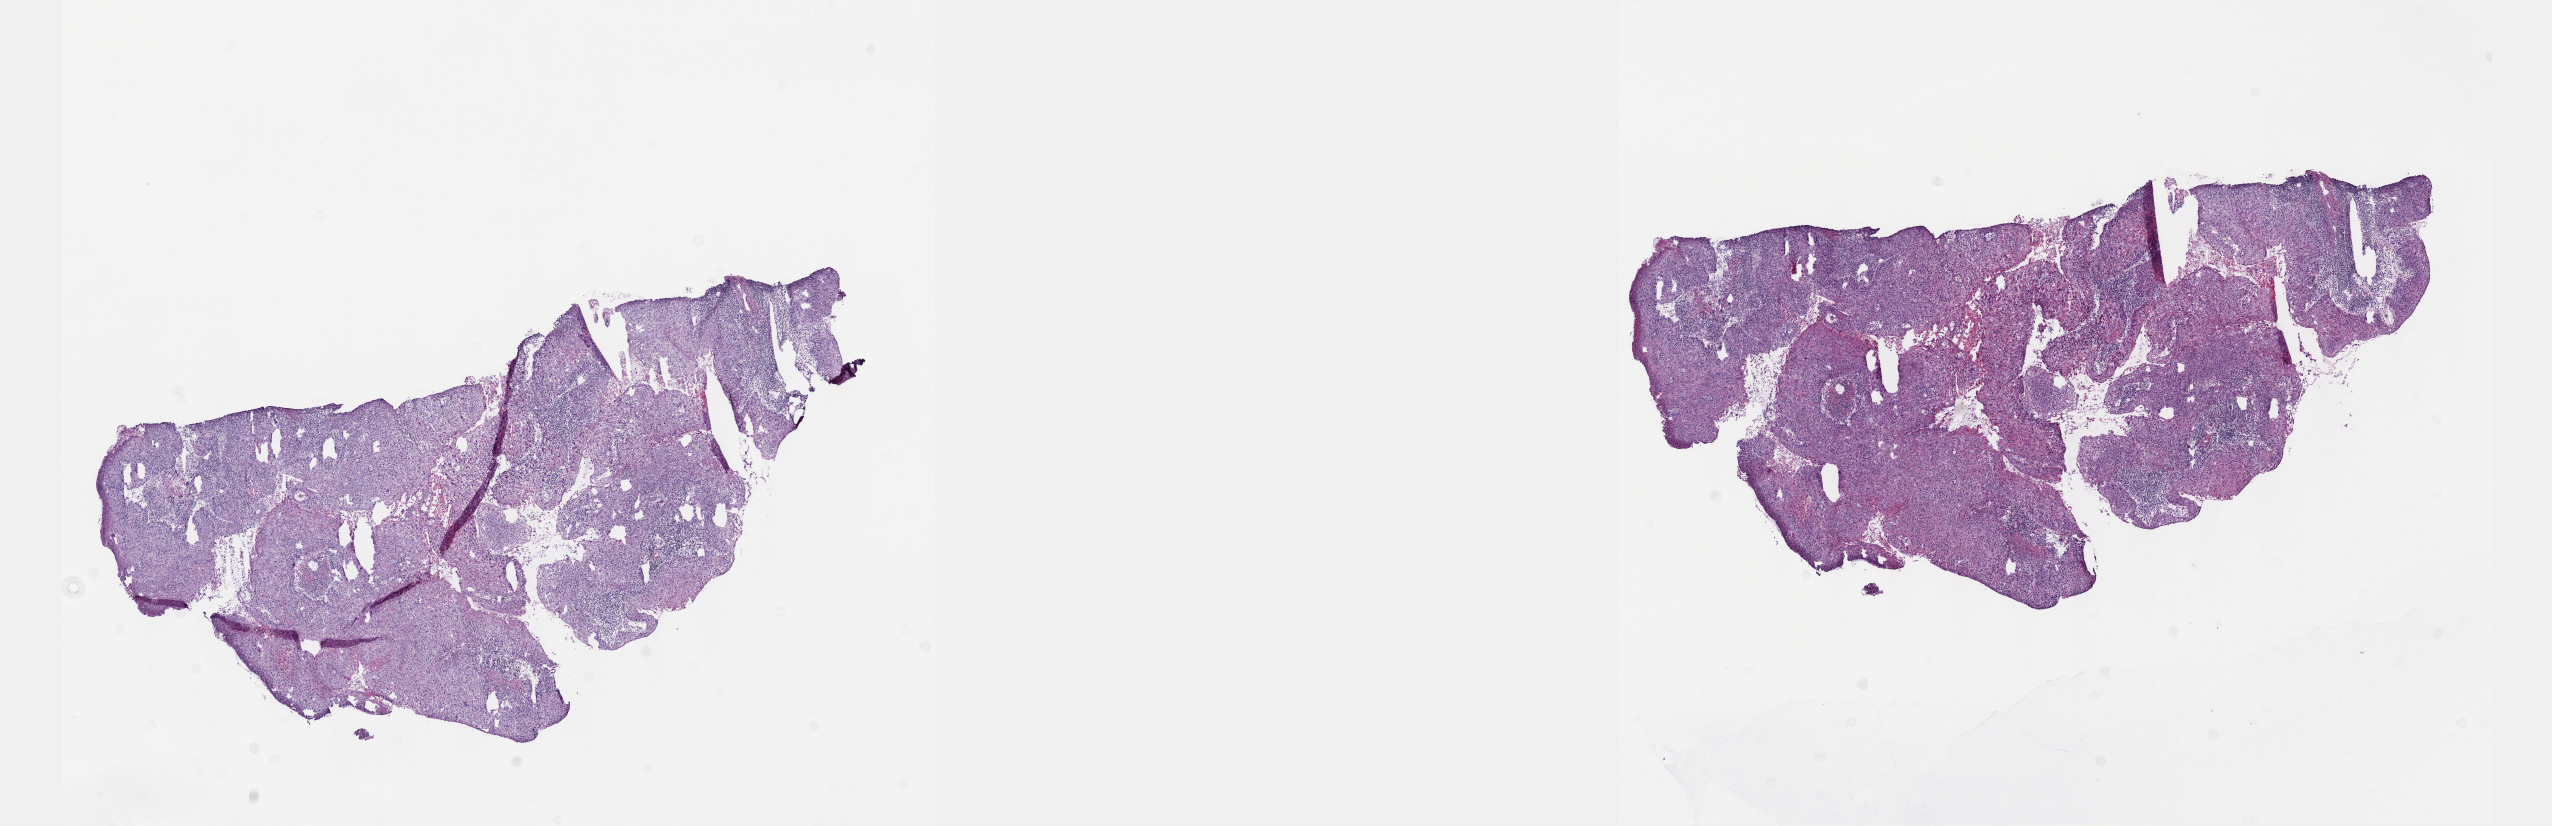
Digitized H&E-stained tissue section (whole slide), whole scanned area (about 20.6 x 6.7 mm, slide scanned at 40x) shown as a low-resolution overview; frozen section from the top of the tissue portion; cervix, primary tumour sample. Patient: female, age at initial diagnosis 76 years. Histologic grade: GX (grade cannot be assessed). Slide review estimates, as recorded: tumour cells 60%, tumour nuclei 60%, normal cells 0%, stromal cells 38%, necrosis 2%. Infiltration values recorded for this section: lymphocyte infiltration 20%, monocyte infiltration 5%, neutrophil infiltration 5%.
FIGO stage: IIB. Histologic diagnosis: Squamous cell carcinoma, NOS (cervix uteri).